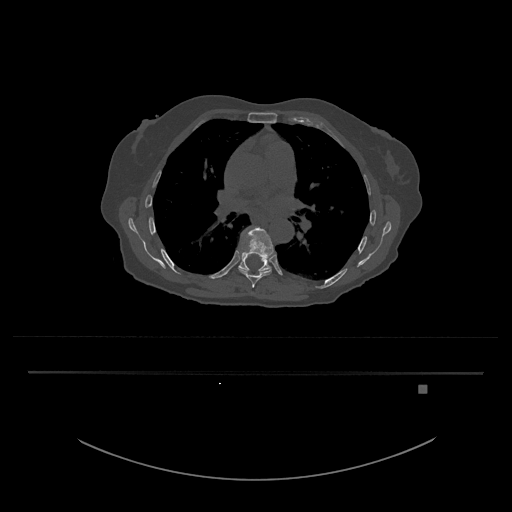
CT including the spine, one axial slice. Position 787 of 797 along the scan axis. Bone window (W 1800 / L 400 HU). 0.5 mm slice thickness. 512 × 512 image matrix, field of view 500 × 500 mm. Patient: female, 57 years. Case-level facts recorded for this patient, not image findings: primary cancer: cervical.
Structures marked on this image (semi-automatically segmented with operator editing):
- T8 vertebra: bounding box [x1, y1, x2, y2] px = [238, 226, 274, 288]
- T9 vertebra: [236, 245, 271, 272]